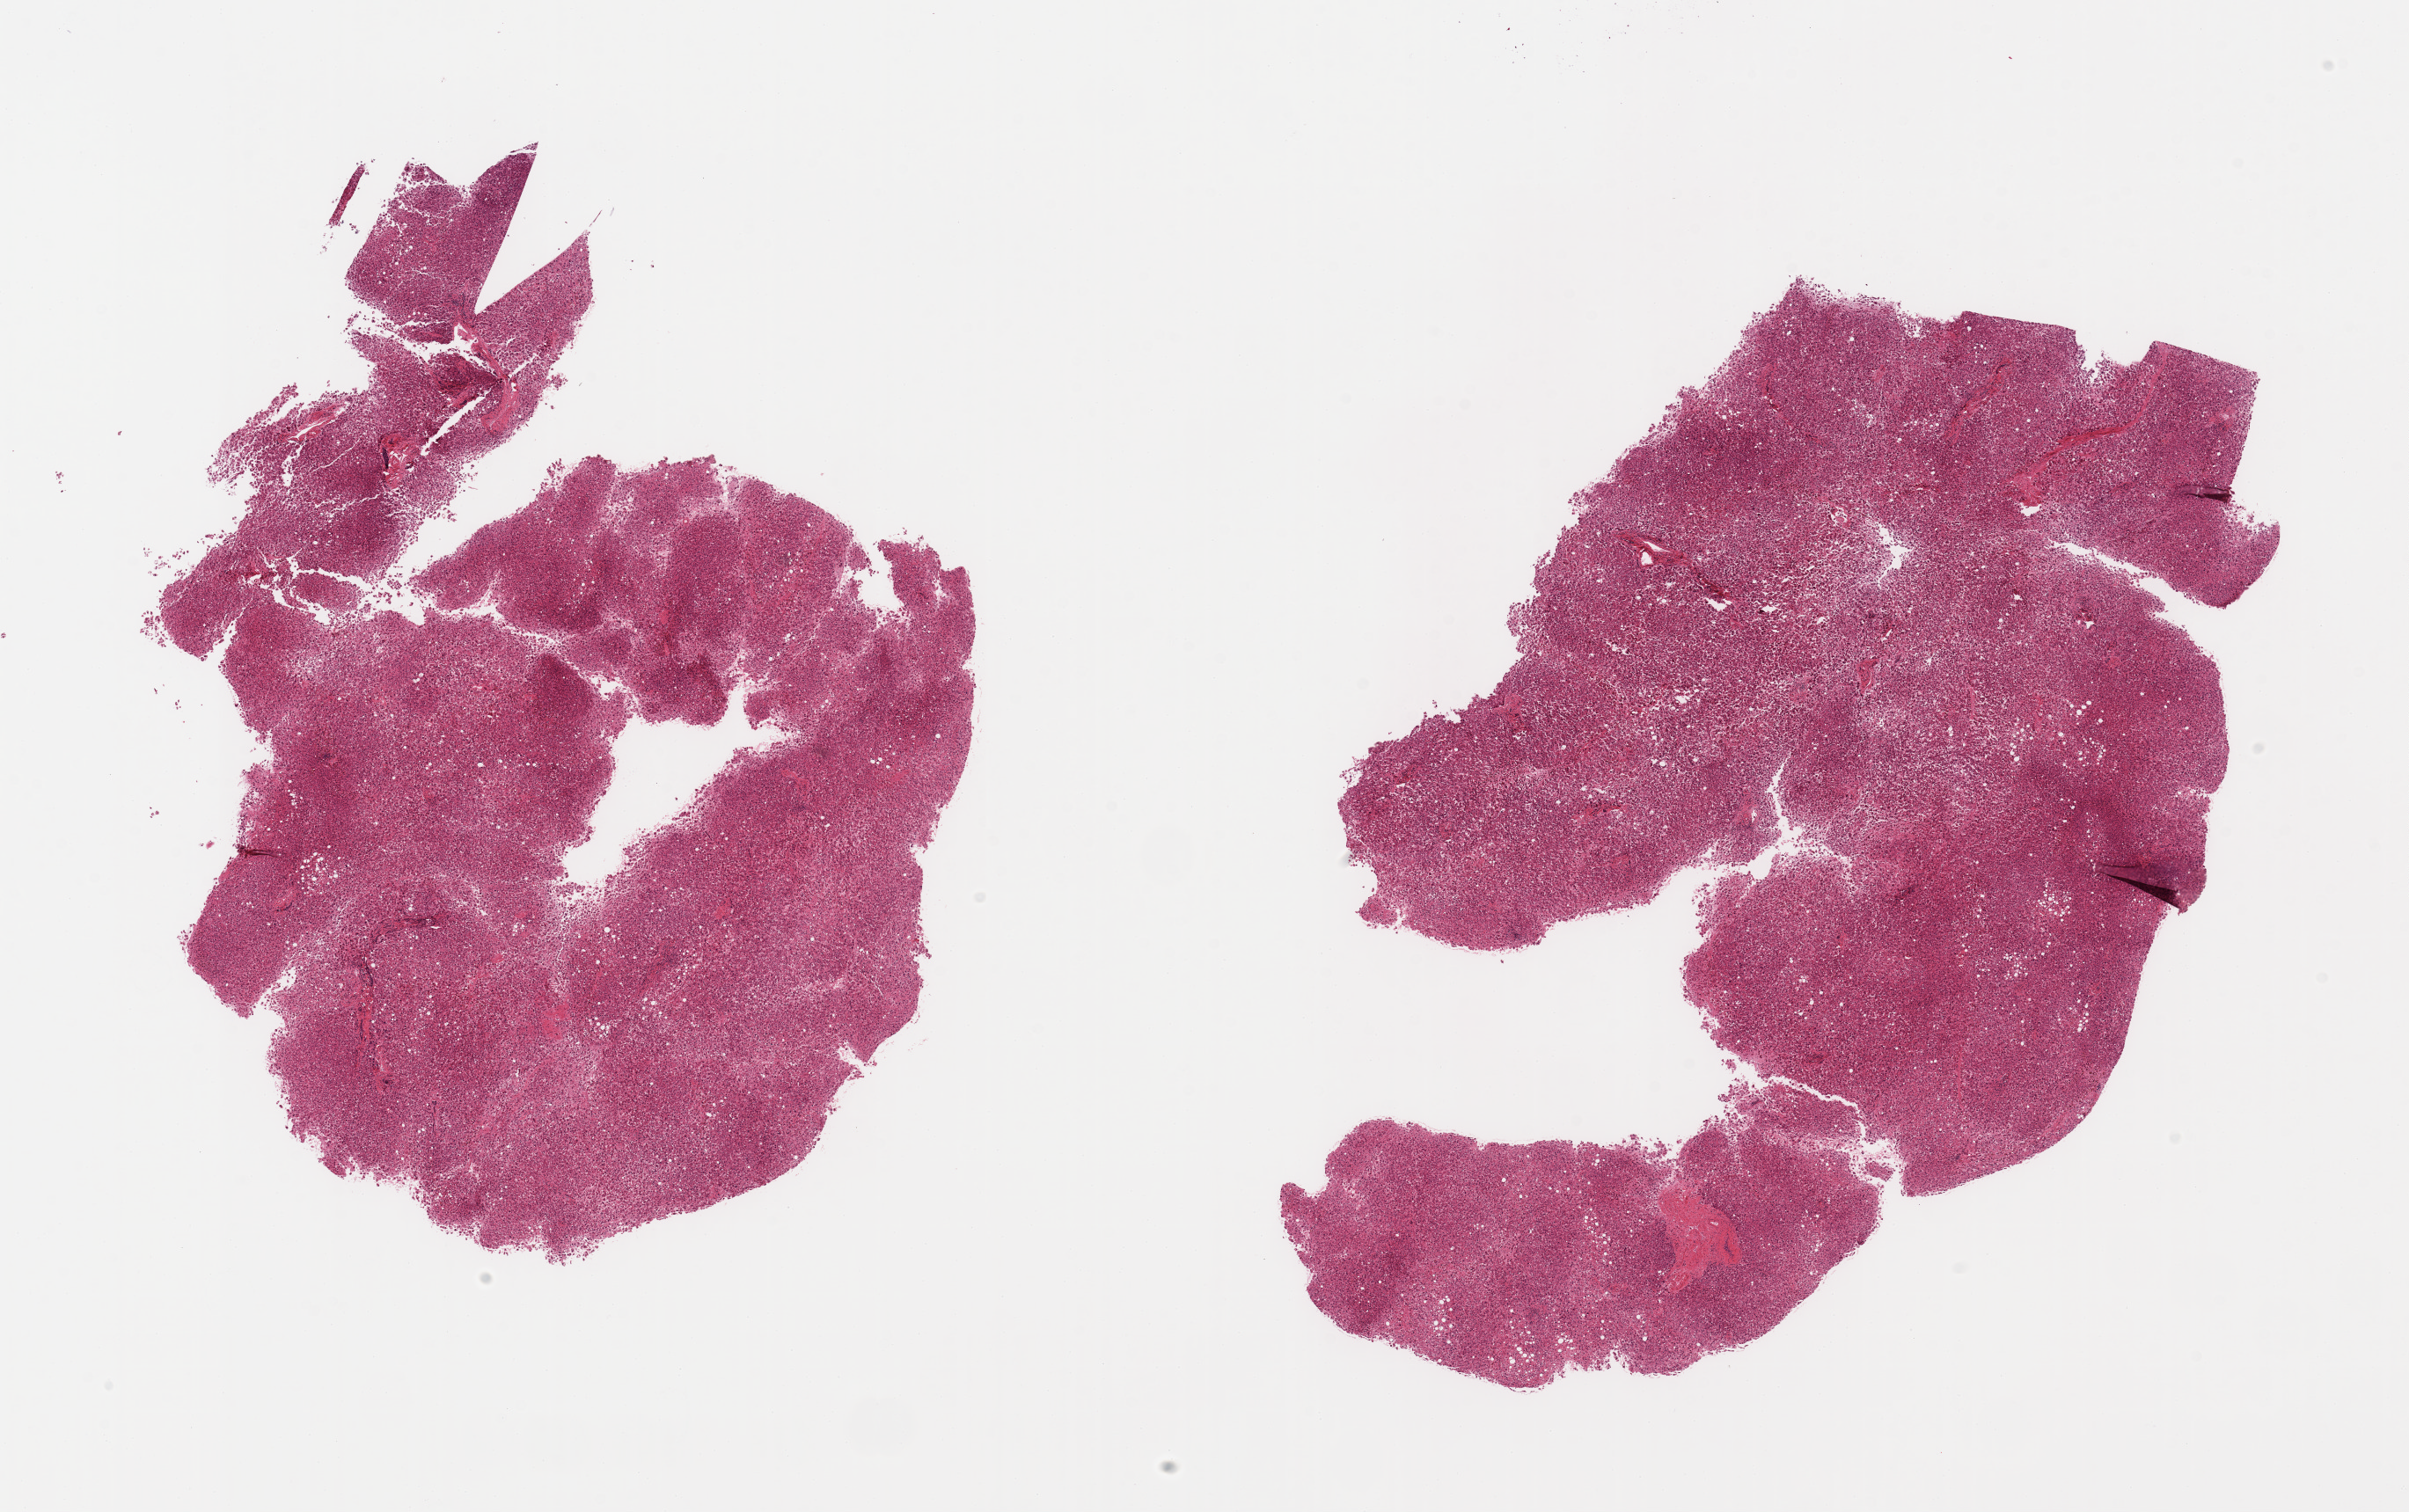
Digitized hematoxylin and eosin (H&E)-stained section — whole scanned area (about 21.7 x 13.6 mm) shown as a low-resolution overview; PAXgene-fixed, paraffin-embedded tissue; section of liver (target tissue); tissue donor sample. Donor: male.
Review note (as recorded): 2 pieces; steatosis, moderate autolysis.